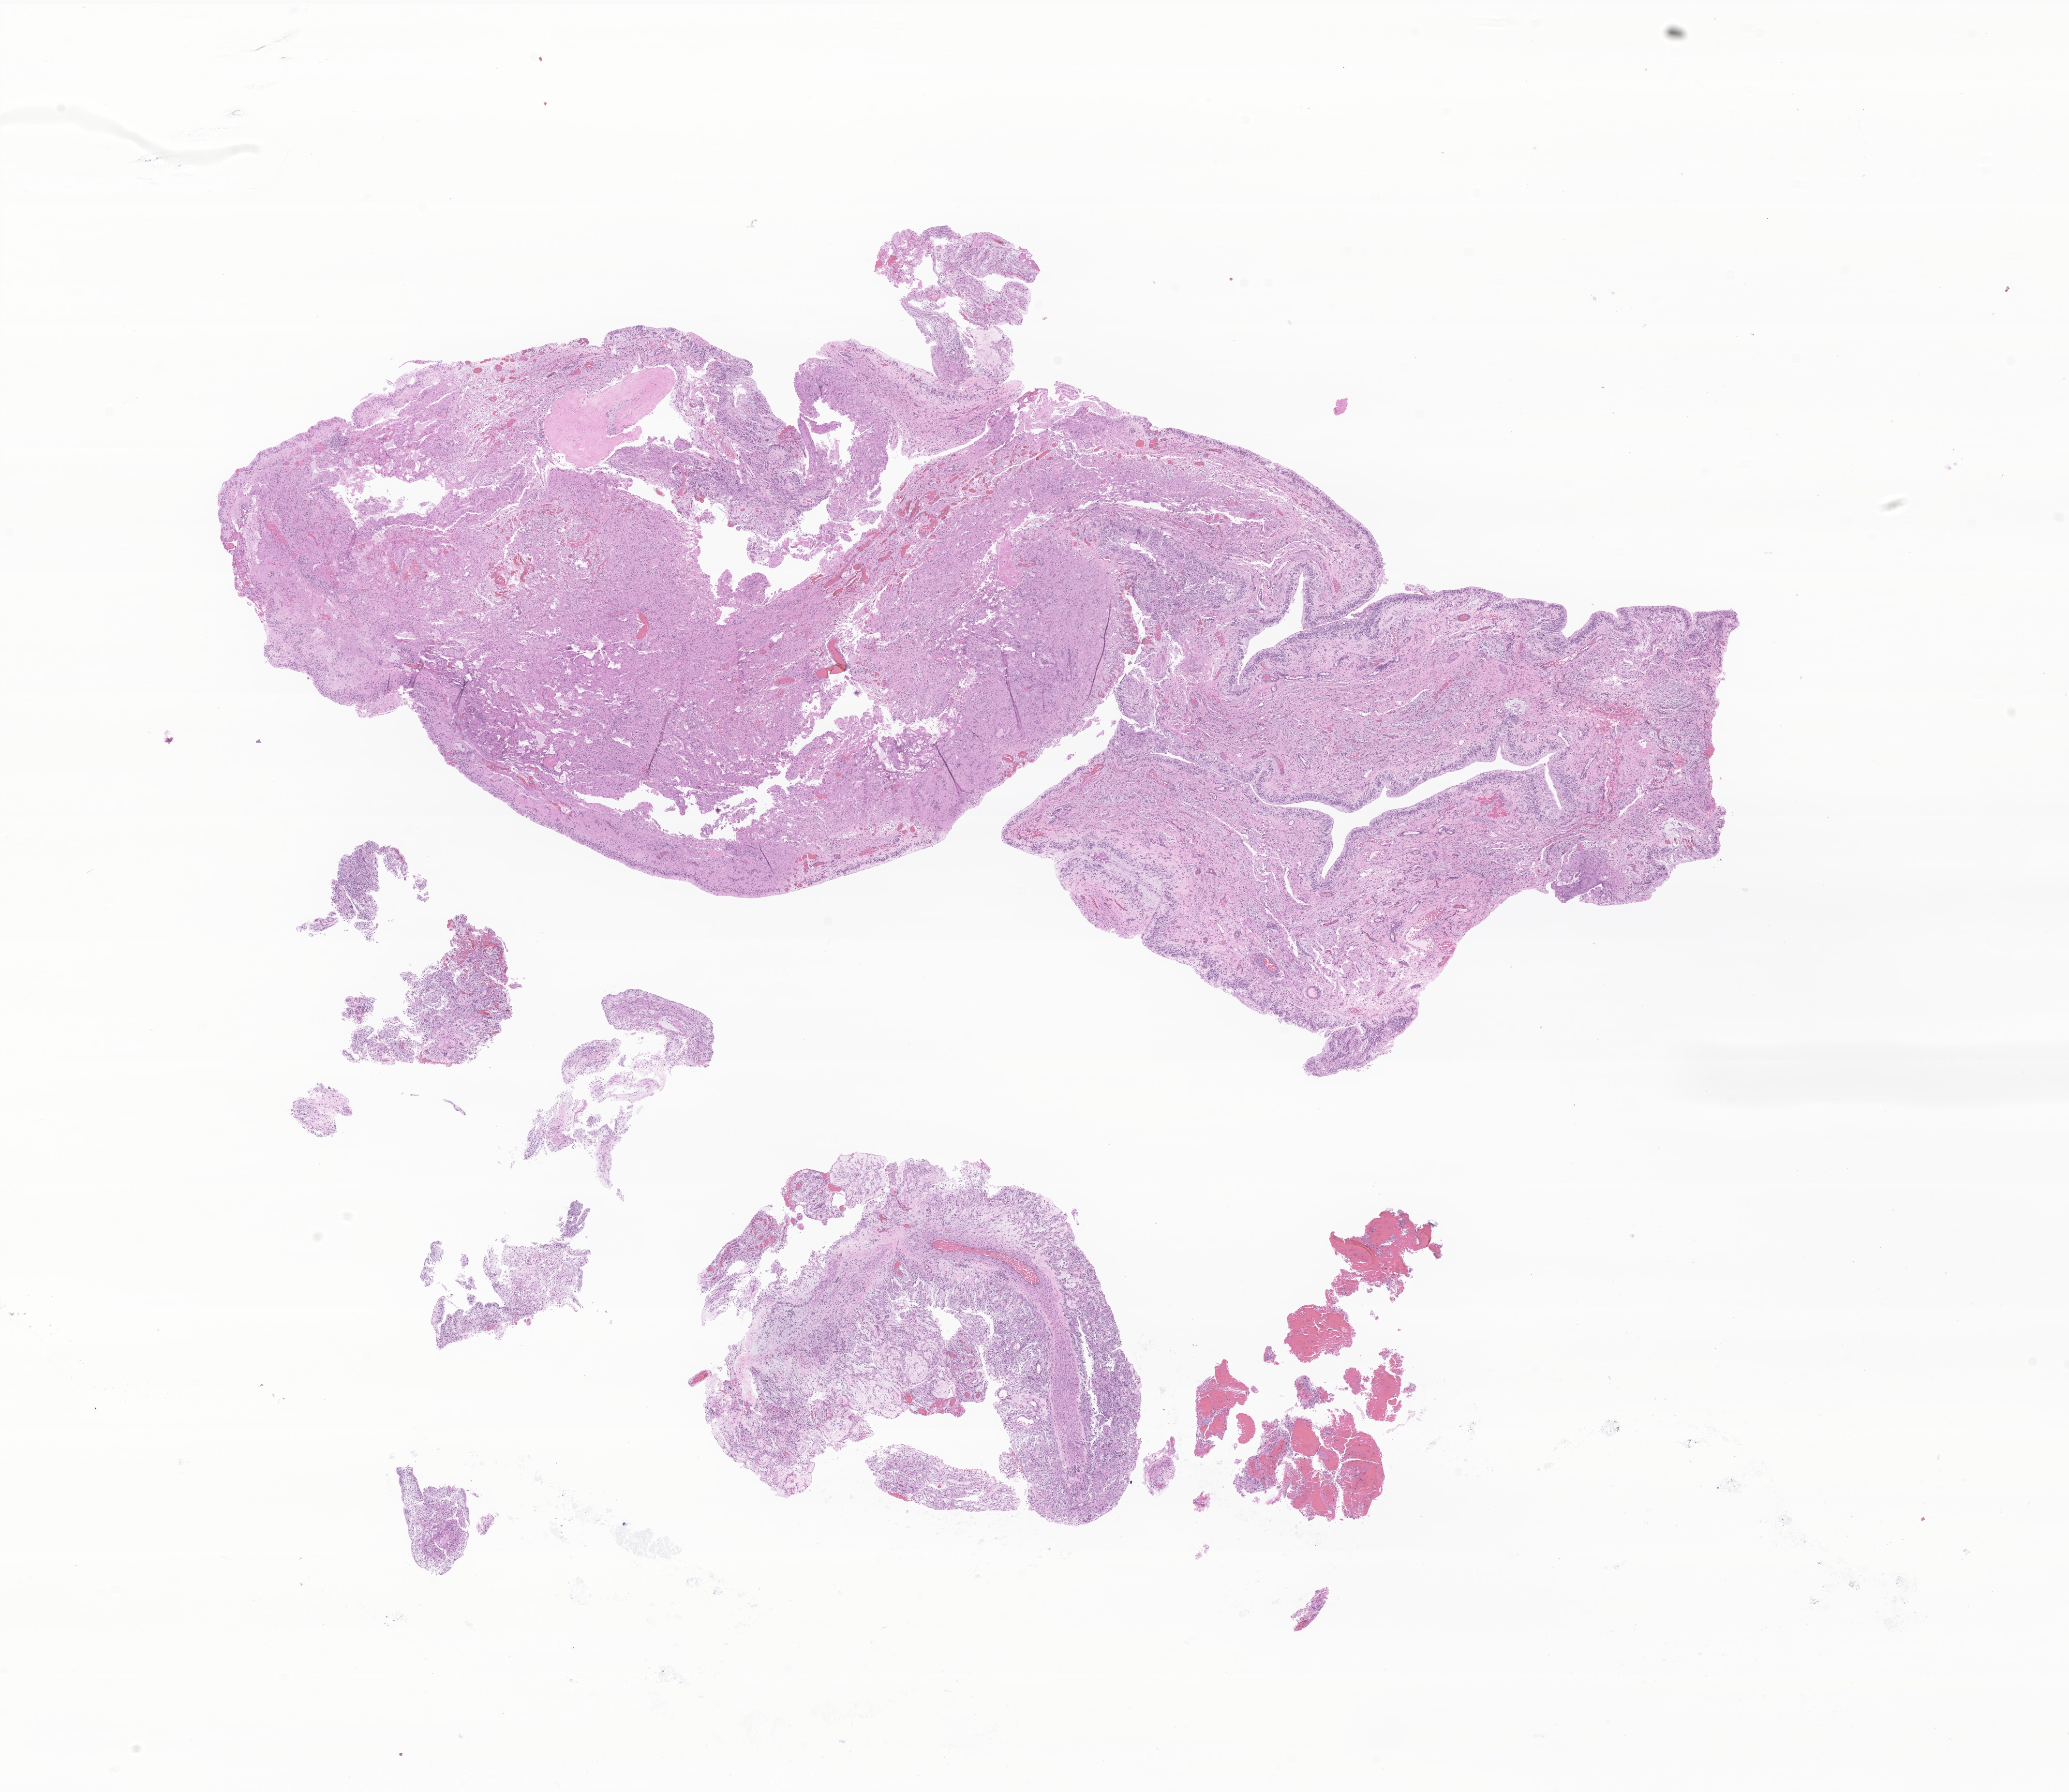
Haematoxylin and eosin whole-slide image of tumor tissue from the brain, whole scanned area (about 18.0 x 15.6 mm) shown as a low-resolution overview, FFPE section. Male patient, age 777 days.
• diagnosis (ICD-O-3 morphology term): Pilocytic astrocytoma